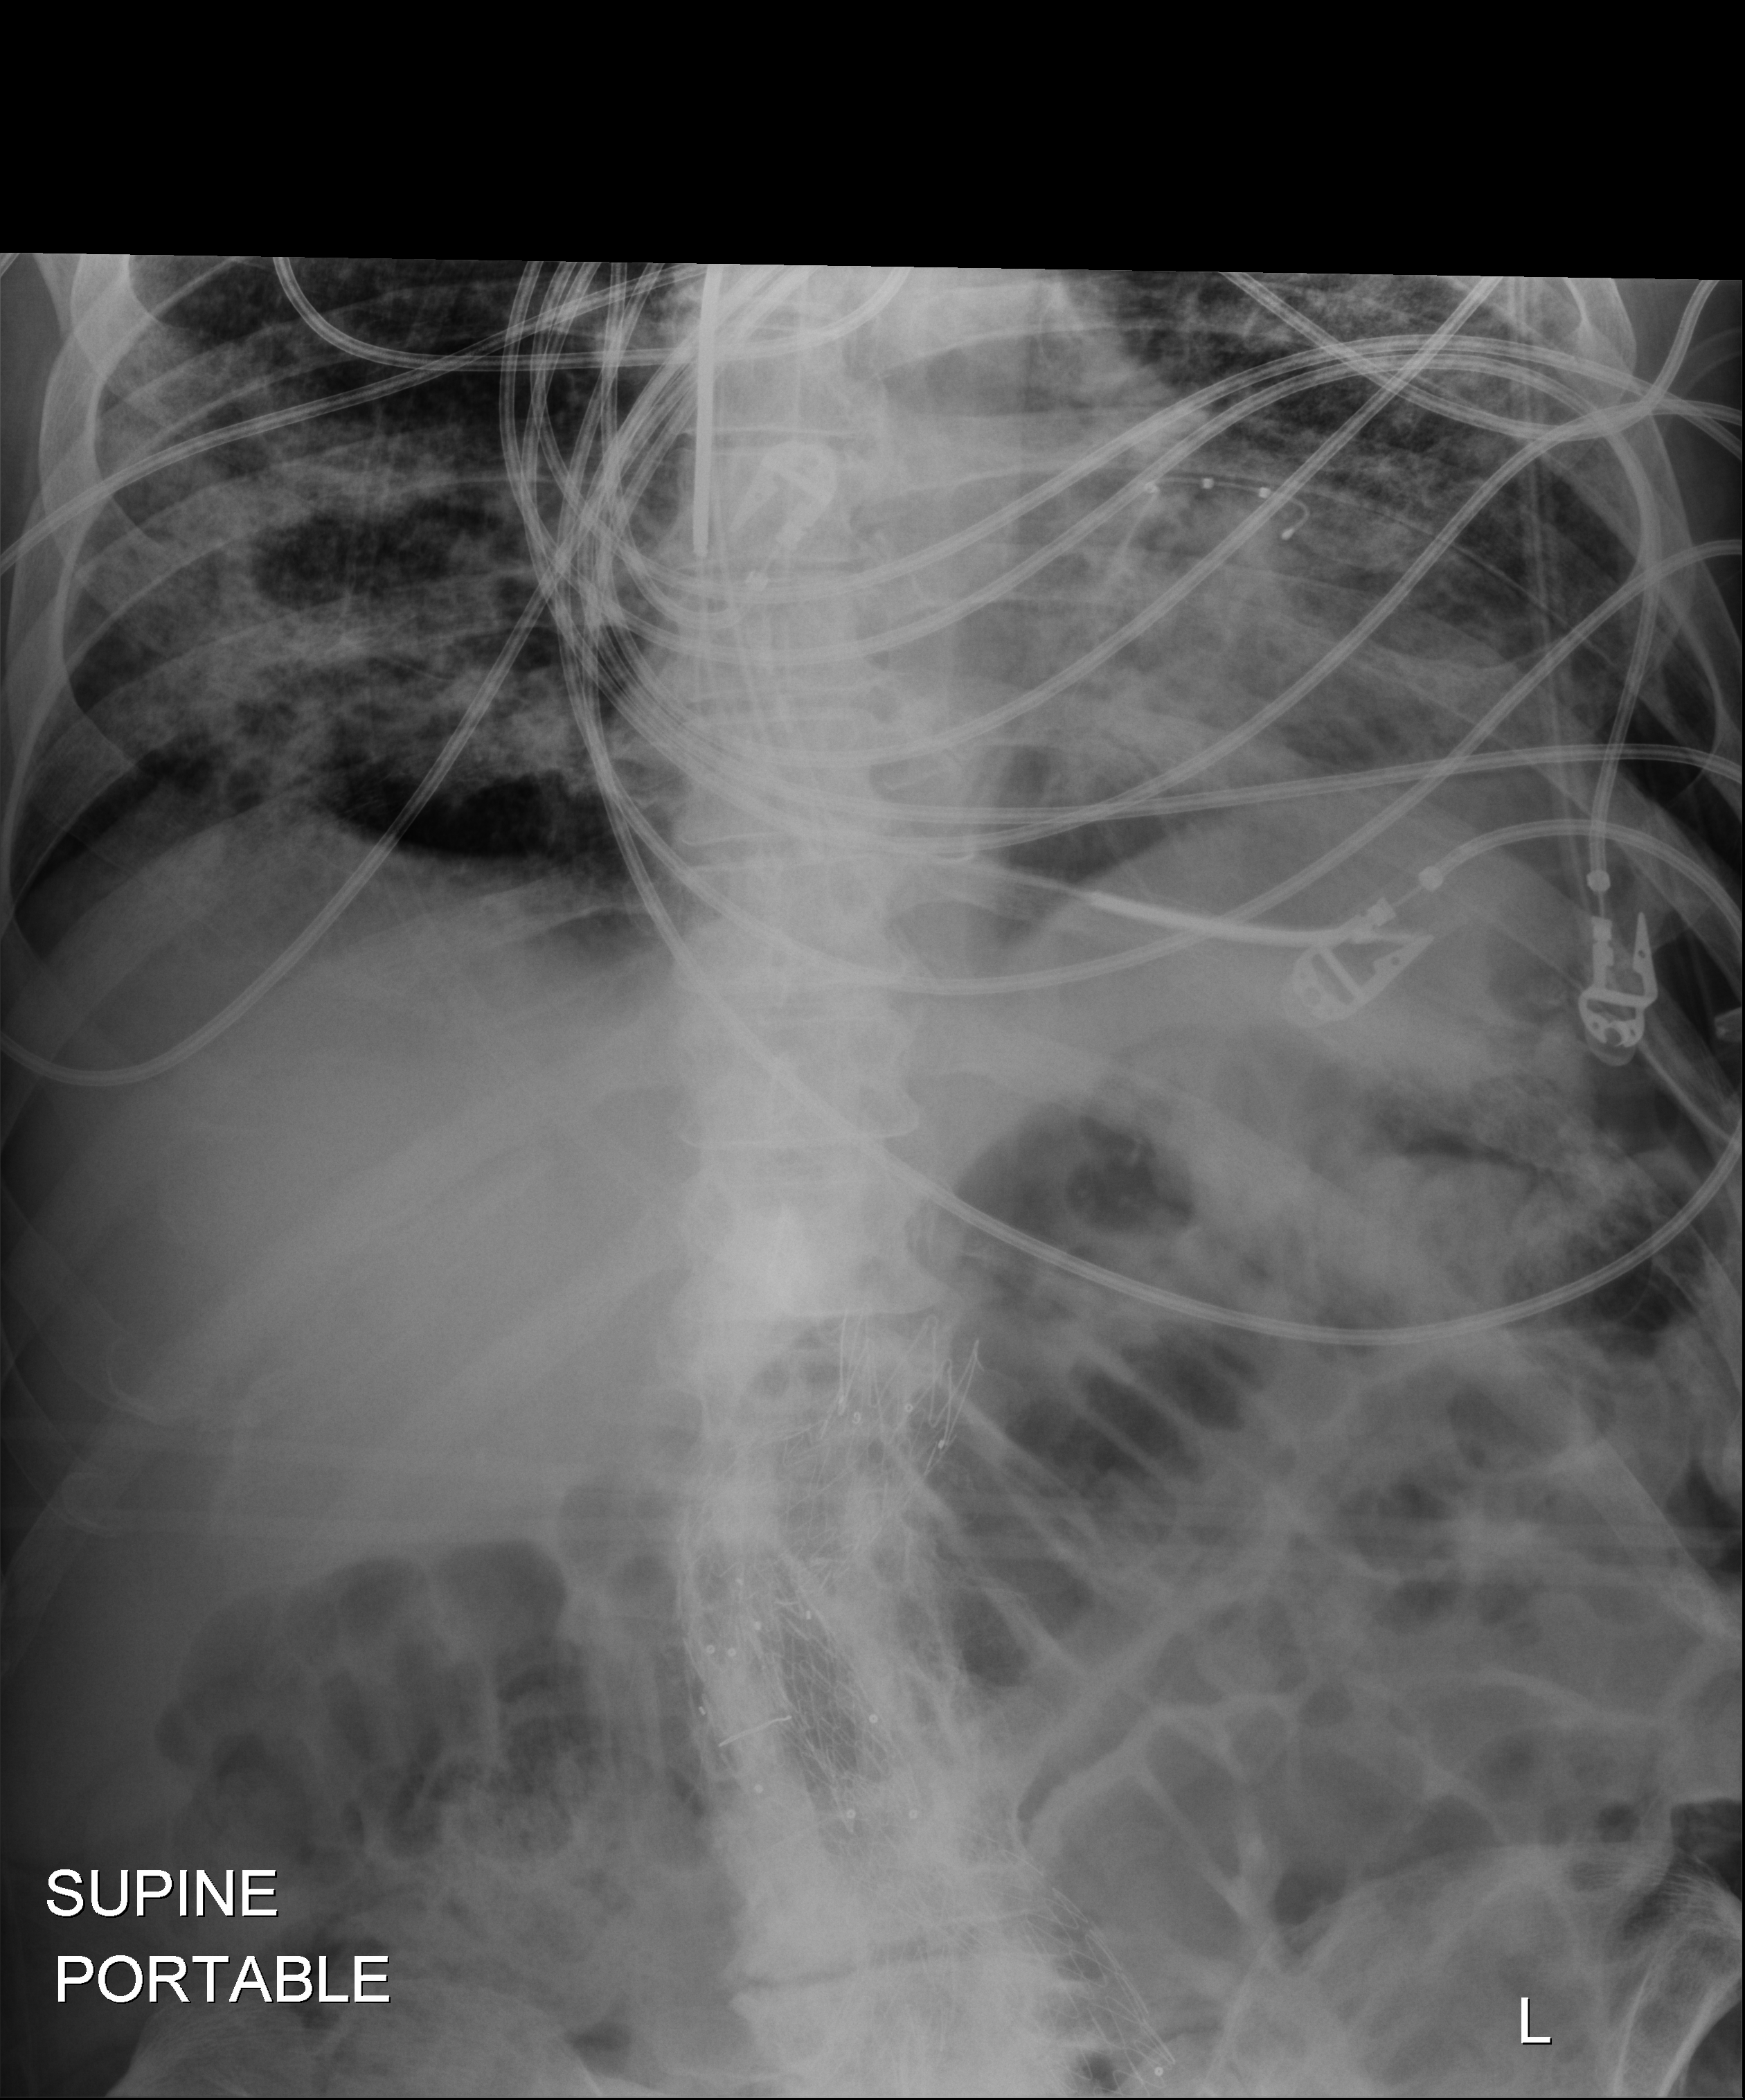
Portable abdomen radiograph, anteroposterior (AP) projection. Patient hospitalised with COVID-19; male, aged 60–74 years.
Hospital-stay facts (about this admission, not read from this image; timing relative to this image not recorded):
- mechanically ventilated during this hospital stay: yes